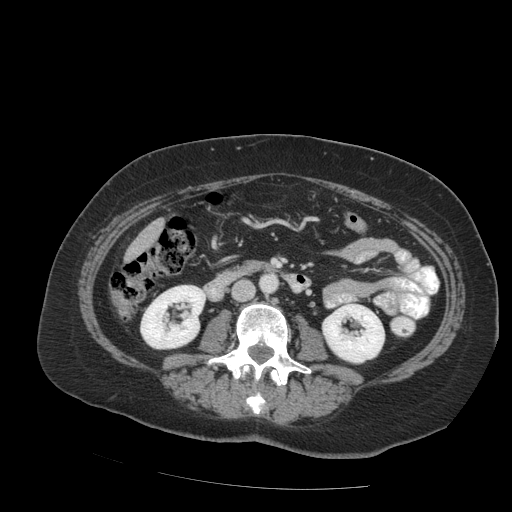
Contrast-enhanced abdominal CT (liver protocol), one axial slice; position 20 of 99 along the scan axis; reconstruction kernel STANDARD; soft-tissue window (W 400 / L 40 HU); 2.5 mm slice thickness; 512 × 512 image matrix, field of view 400 × 400 mm. Case-level facts recorded for this patient, not image findings: diagnosis: hepatocellular carcinoma (patient treated with transarterial chemoembolisation; whether this scan precedes or follows treatment is not stated here); TNM stage (as recorded): Stage-IVB; Child-Pugh class: A; tumour nodularity: uninodular.
Structures marked on this image (semi-automatically segmented with operator editing):
- liver parenchyma outside the tumour (the mass and vessels are separate outlines, so this box may not span the whole liver): bounding box [x1, y1, x2, y2] px = [126, 218, 164, 258]